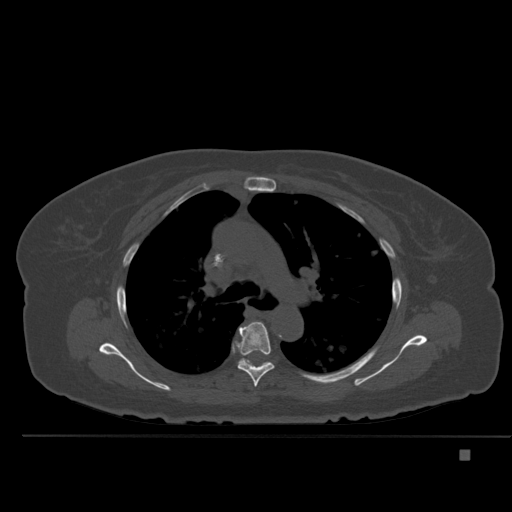
CT including the spine, one axial slice. Bone window (W 1800 / L 400 HU). 1.5 mm slice thickness. 512 × 512 image matrix. Female patient, age 74 years. From the clinical record (not read from this slice): primary cancer: colon.
Structures marked on this image (semi-automatically segmented with operator editing):
- T5 vertebra: box from (x=235, y=321) to (x=274, y=387) px
- T6 vertebra: (x=232, y=345)–(x=270, y=363)